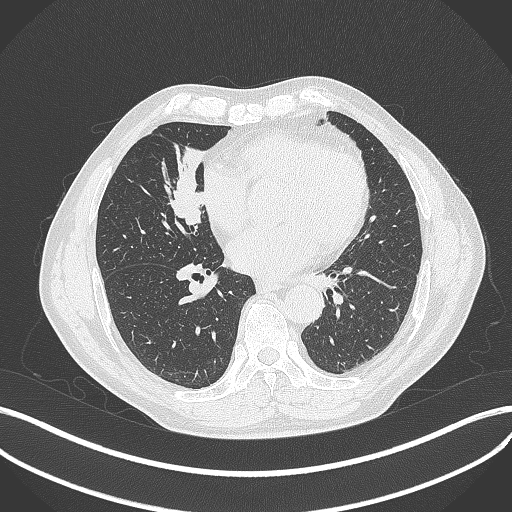
Chest CT, one axial slice. Slice 170 of 429 in the series (ordered by position). Reconstruction kernel B70f. Lung window (W 1500 / L -600 HU). 1 mm slice thickness. 512 × 512 image matrix. Patient: male, 61 years. Case-level facts recorded for this patient, not image findings: clinical TNM (as recorded): T2b N1 M0.
Outlined on this slice (bounding box drawn by a radiologist):
- lung tumour (recorded histology: squamous cell carcinoma): box from (x=155, y=139) to (x=215, y=236) px